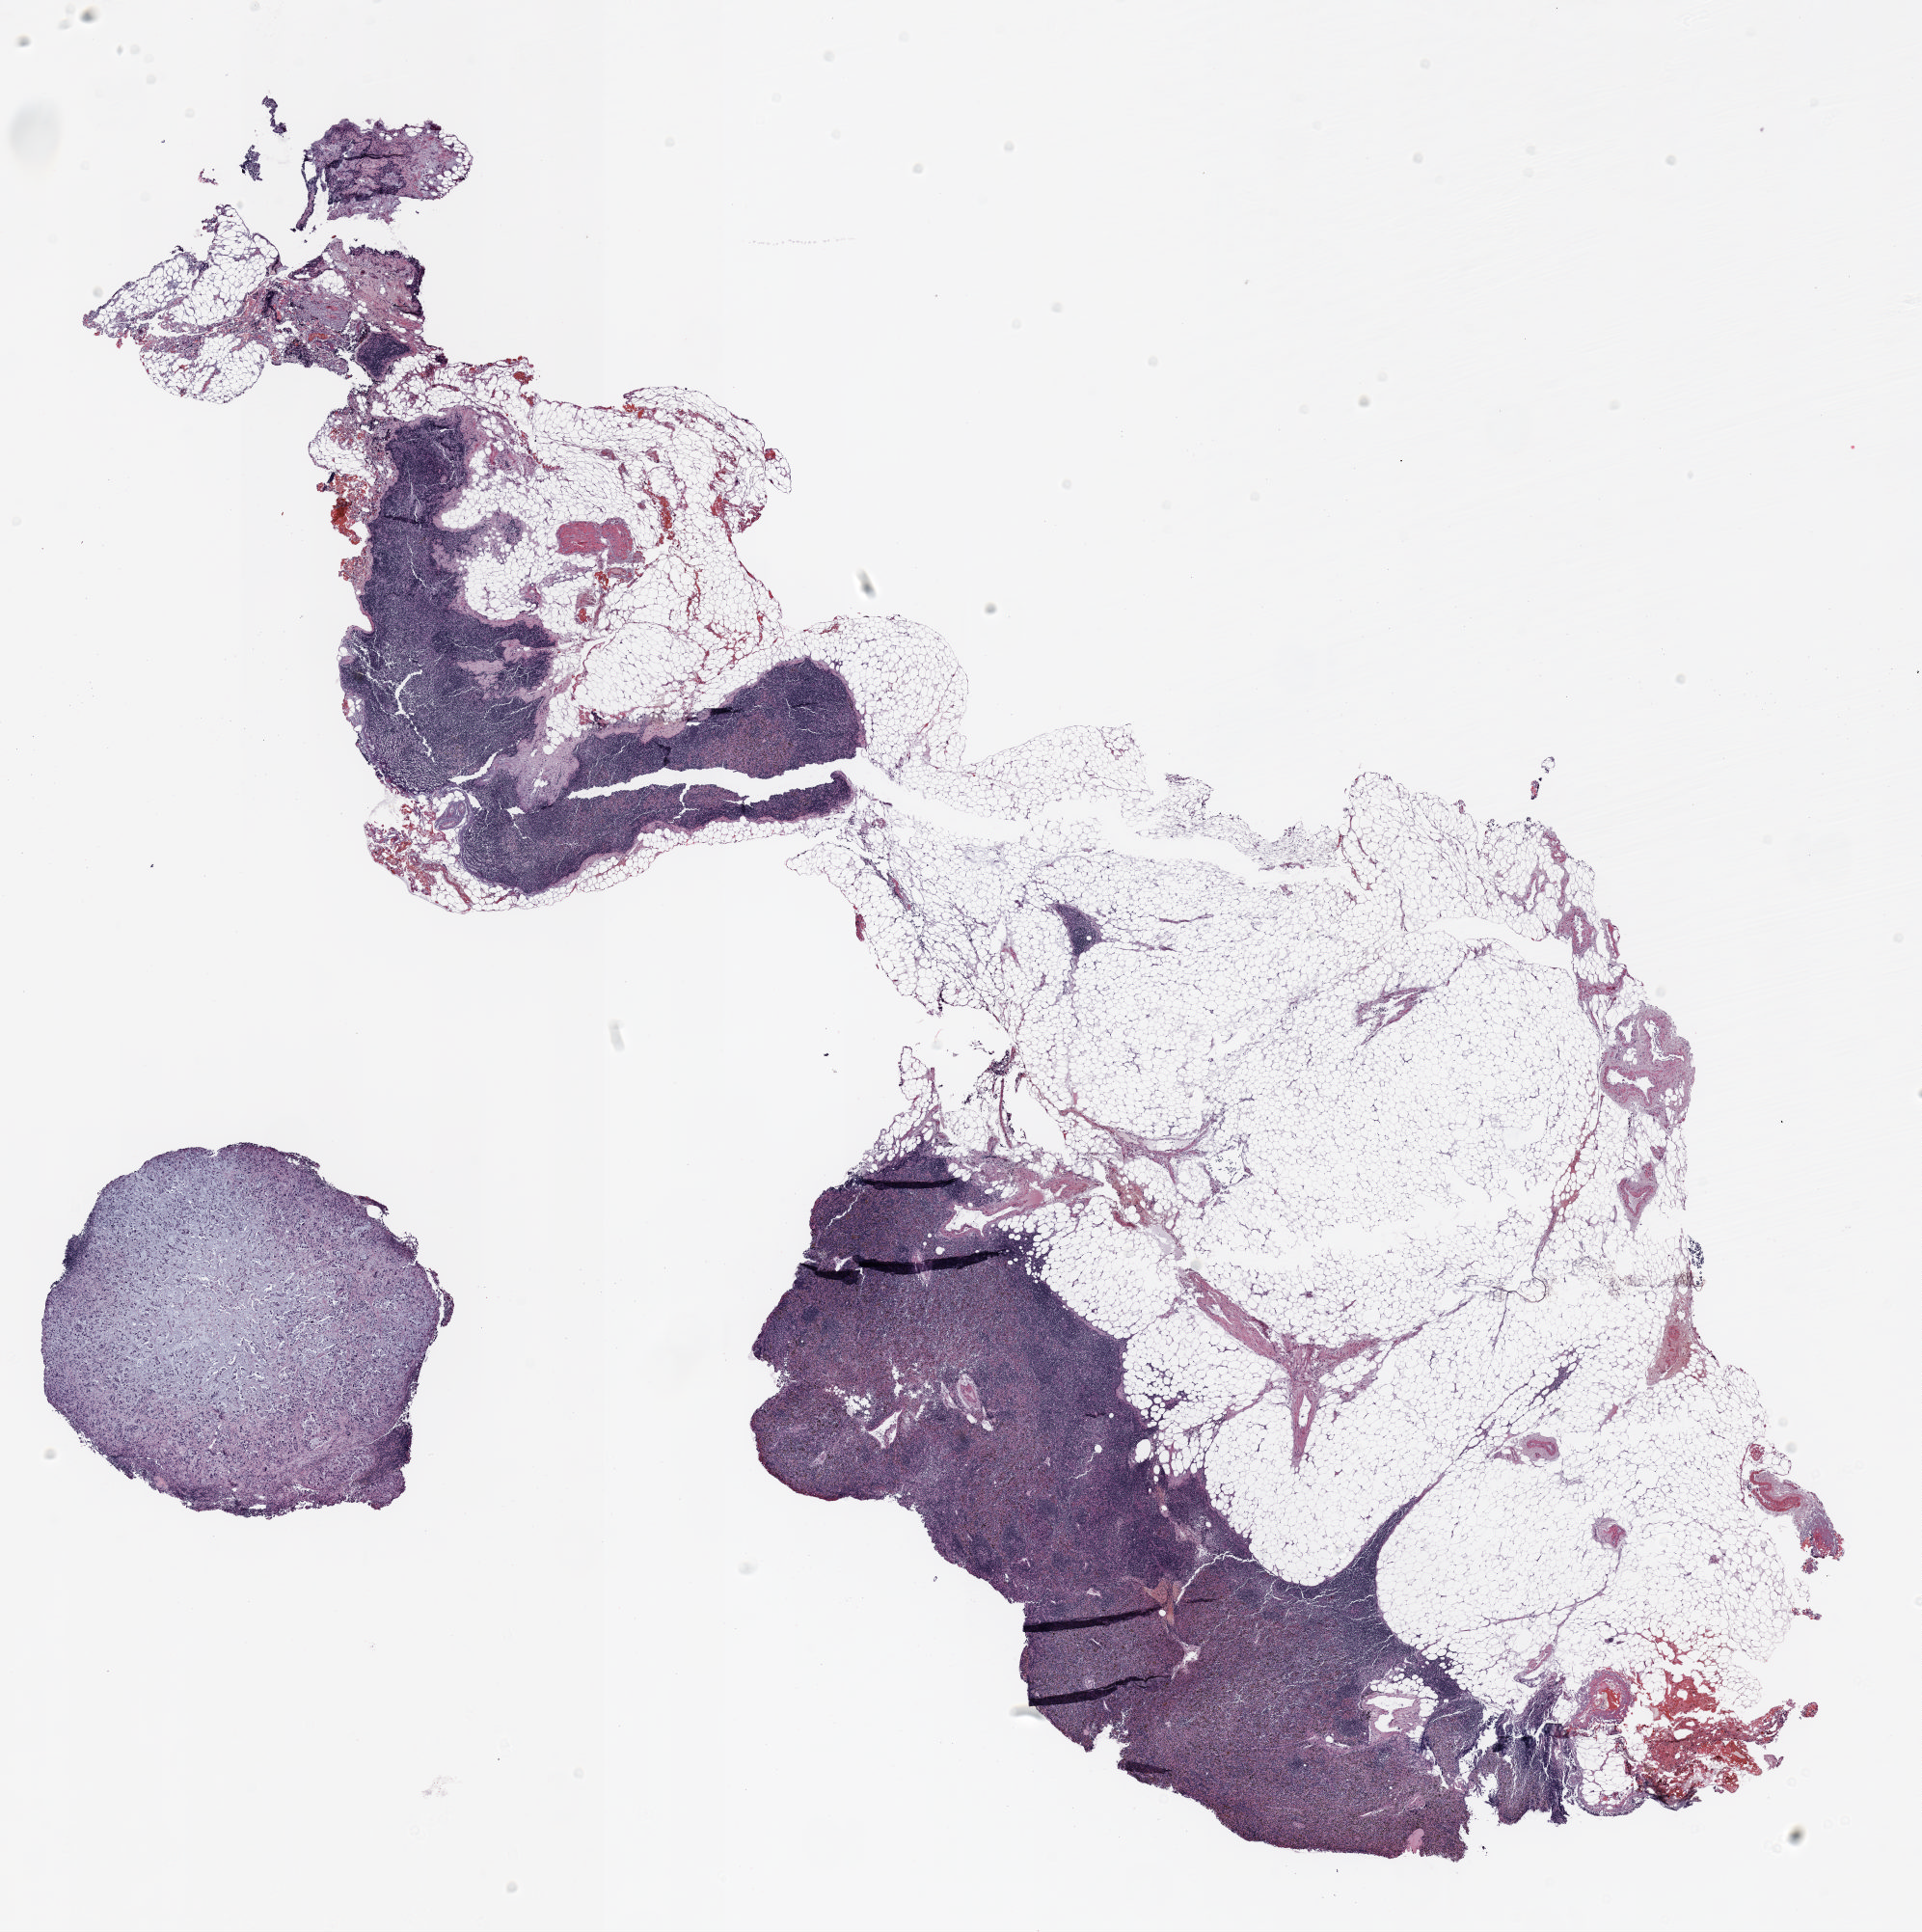
Whole-slide histology image, Hematoxylin and eosin (H&E) stained — whole scanned area (about 16.0 x 16.1 mm, slide scanned at 20x) shown as a low-resolution overview. Formalin-fixed paraffin-embedded (FFPE) section. Lung tissue. Female patient, aged 58 at enrolment. Former smoker at enrolment. Grade: poorly differentiated (G3).
• stage (AJCC 6th edition): IIIA
• tumour size (pathology): 50 mm
• primary tumour location (clinical record): left lower lobe
• participant's lung-cancer diagnosis: Large cell carcinoma, NOS (ICD-O-3 8012/3)